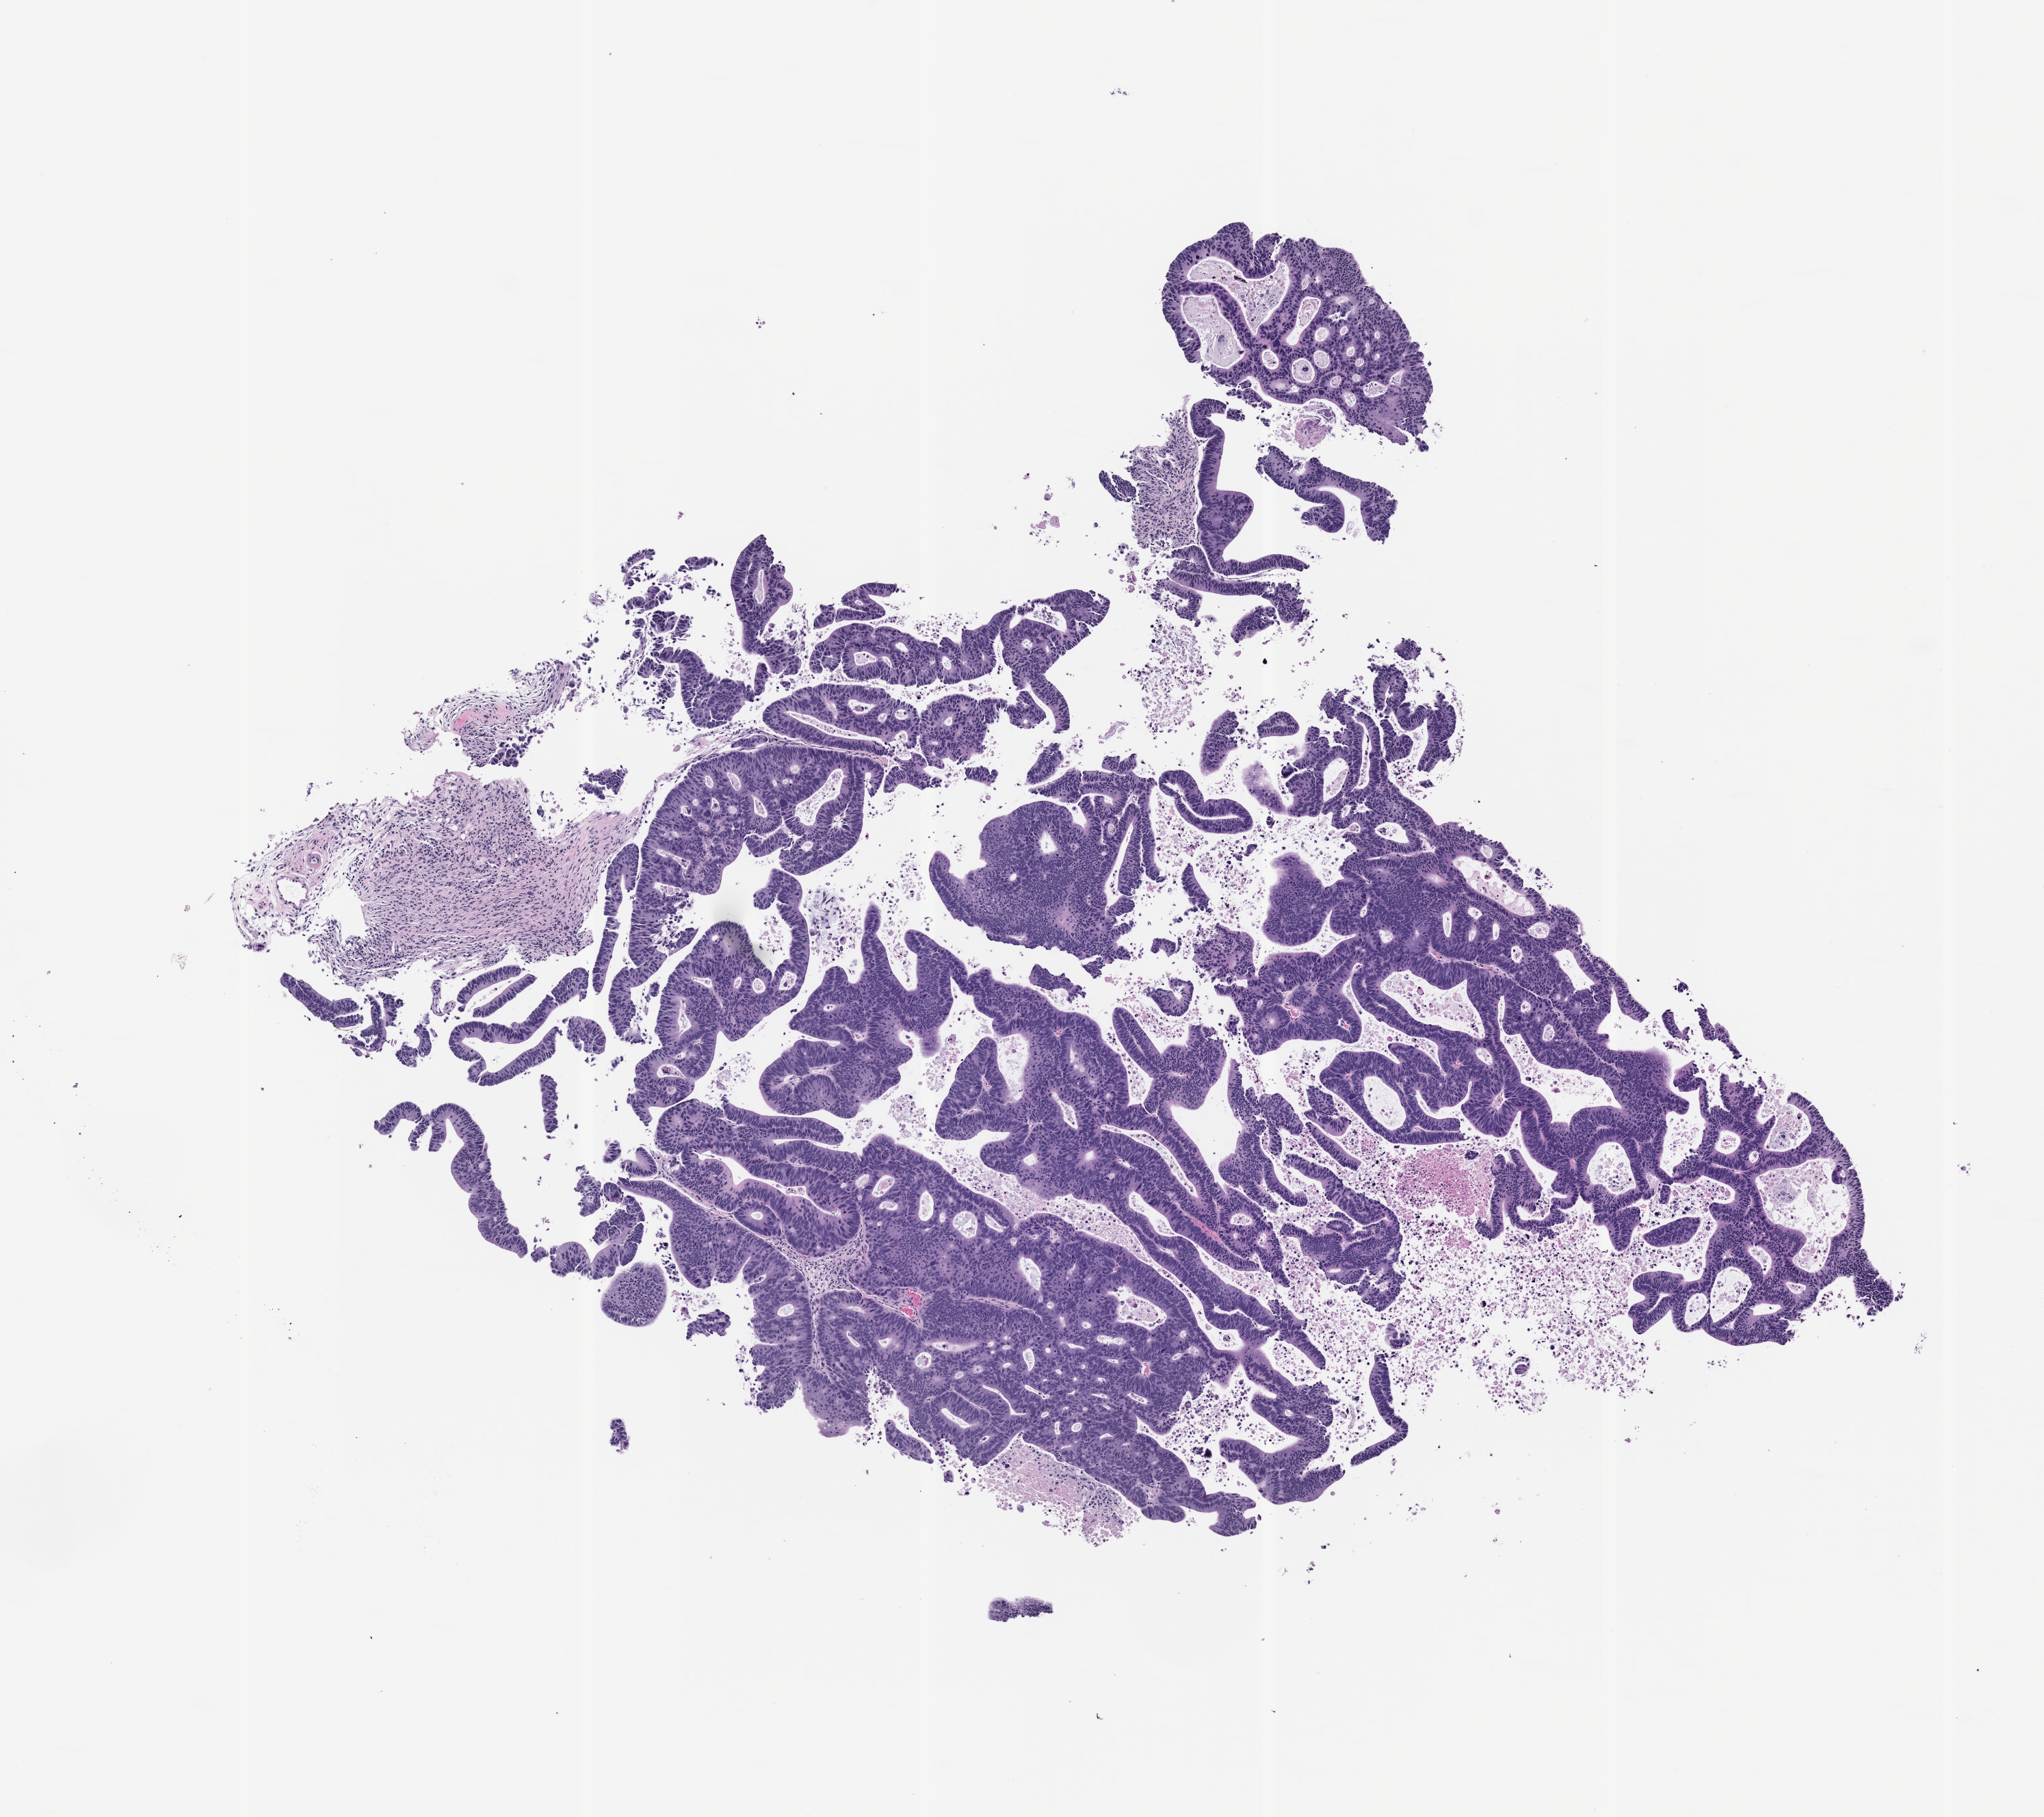
Whole-slide image, haematoxylin and eosin: patient-derived xenograft (human tumor grown in a mouse), passage 2, a low-resolution overview of the entire scanned area, about 6.0 x 5.3 mm. Formalin-fixed paraffin-embedded section. Originating tumor site category: colon.
- originating patient diagnosis: Colon Adenocarcinoma